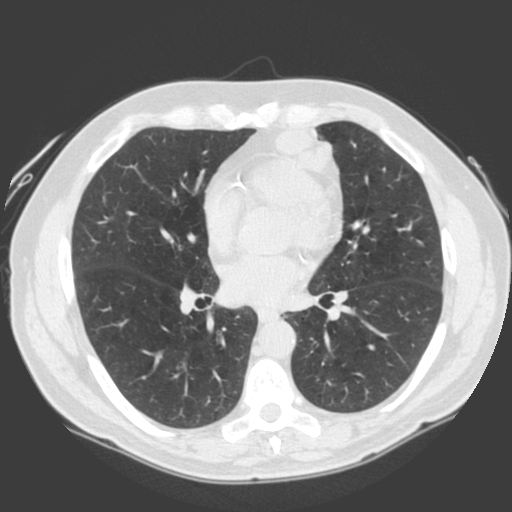
Low-dose screening chest CT, one axial slice. Slice 90 of 185 in the series (ordered by position). Lung window (W 1500 / L -600 HU). 2 mm slice thickness. 512 × 512 image matrix, field of view 360 × 360 mm.
Annotated regions visible in this slice (expert manual segmentation):
- lesion 1 (tumor, lower lobe of left lung): bounding box <275,124,336,176> (left, top, right, bottom; pixels)